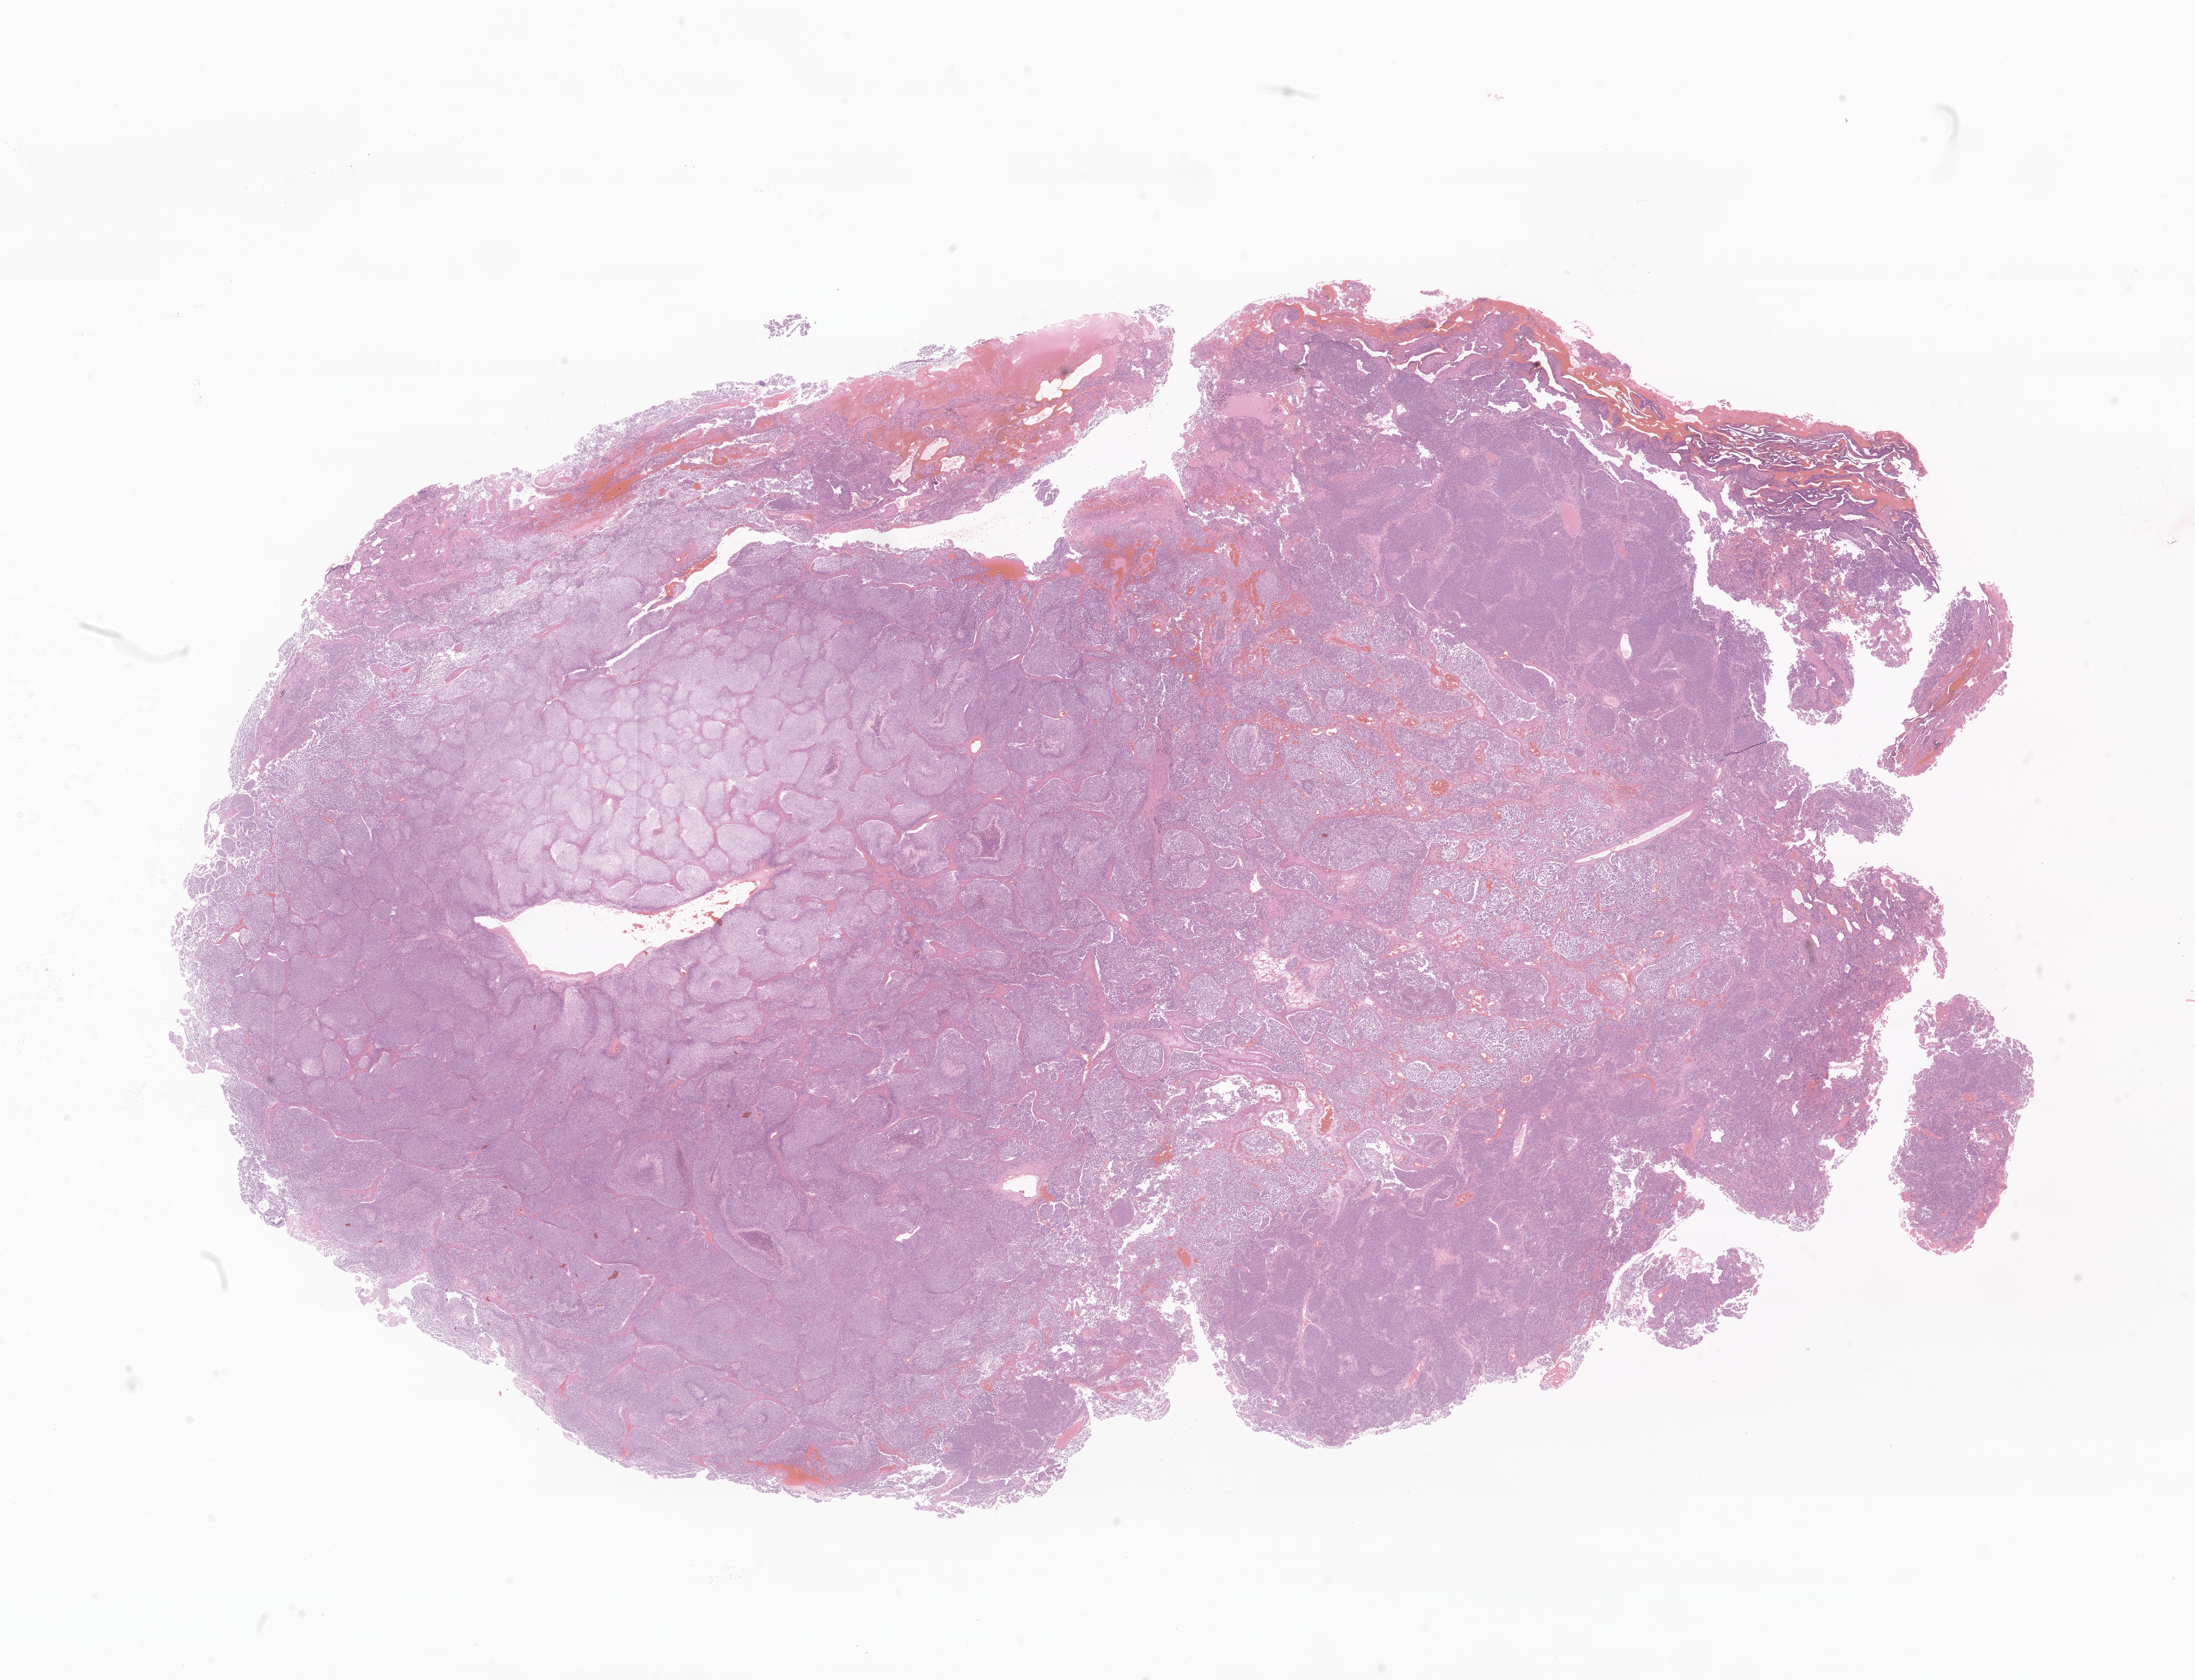
Digitized haematoxylin and eosin-stained section of tumor tissue from the cerebellum, whole scanned area (about 25.1 x 19.2 mm) shown as a low-resolution overview; formalin-fixed paraffin-embedded section. Patient male; age 71 months.
• diagnosis (ICD-O-3 morphology term): Medulloblastoma, NOS